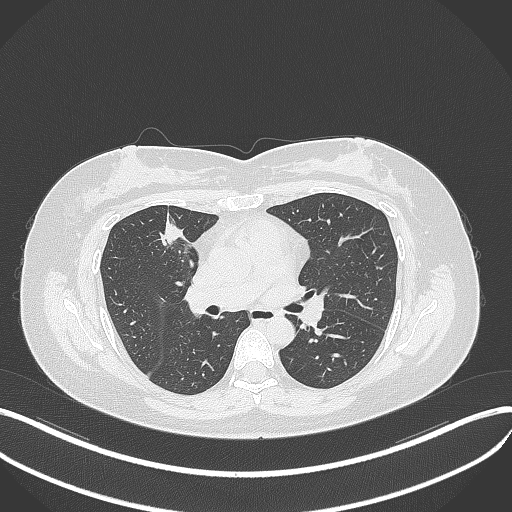
Chest CT, one axial slice; slice 178 of 273 in the series (ordered by position); 120 kVp; lung window (W 1500 / L -600 HU); 1 mm slice thickness; 512 × 512 image matrix, field of view 400 × 400 mm. Female patient, age 42 years. From the clinical record (not read from this slice): clinical TNM (as recorded): T1b N0 M0.
Outlined on this slice (bounding box drawn by a radiologist):
- lung tumour (recorded histology: adenocarcinoma): bounding box (x1, y1, x2, y2) in pixels: (155, 211, 187, 250)